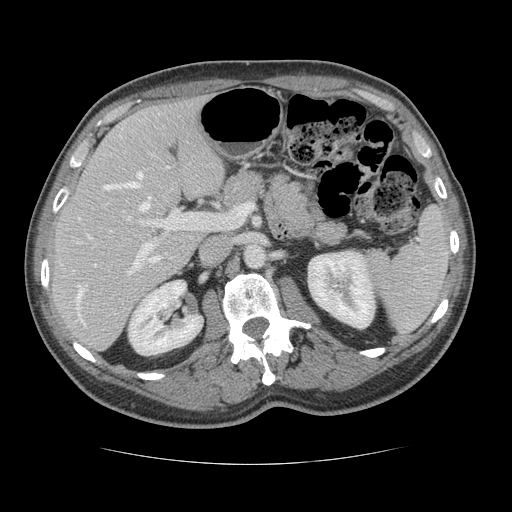
Contrast-enhanced abdominal CT, one axial slice. Slice 74 of 134 in the series (ordered by position). Reconstruction kernel STANDARD. 120 kVp. Soft-tissue window (W 400 / L 40 HU). 2.5 mm slice thickness. 512 × 512 image matrix. Male patient, age 68 years. Case-level facts recorded for this patient, not image findings: diagnosis: colorectal cancer liver metastases, imaged before liver resection; multiple liver metastases: yes; largest metastasis: 2.2 cm.
Outlined on this slice (expert manual segmentation):
- hepatic veins: bounding box <77,172,151,324> (left, top, right, bottom; pixels)
- liver: <51,100,224,350>
- planned liver remnant (the part of the liver to remain after resection): <52,99,224,337>
- portal vein (with intrahepatic branches): <127,165,197,273>